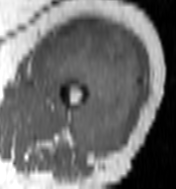
MRI of an extremity soft-tissue mass, one axial slice; position 66 of 100 along the scan axis; MR volume resampled by the dataset authors to the PET/CT grid (not the native acquisition matrix); 176 × 189 image matrix, field of view 172 × 185 mm. Female patient. Case-level facts recorded for this patient, not image findings: histological type: undifferentiated – high grade; grade: high; site of the primary tumour: left thigh.
Structures marked on this image (expert contour drawn on MRI and transferred to this co-registered scan by the dataset authors):
- gross tumour volume including surrounding oedema: bounding box <46,23,143,156> (left, top, right, bottom; pixels)
- gross tumour volume (mass): <46,23,141,156>